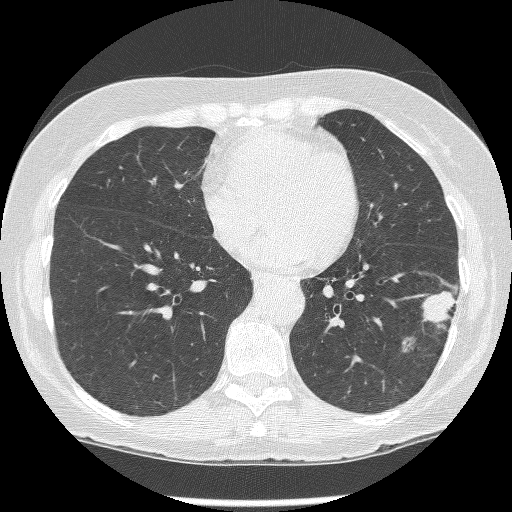
Low-dose screening chest CT, axial slice, baseline annual screen, lung window (W 1500 / L -600 HU), 1.25 mm slice thickness. Female, age 62 years at enrolment. Former smoker at enrolment.
• Lesion marked by an expert reader, bounding box <415,283,460,340> (left, top, right, bottom; pixels).
• The screening reader recorded 2 non-calcified nodules or masses ≥4 mm on this exam (left lower lobe, left lower lobe); which of them this box marks is not recorded.
• Lung cancer was diagnosed 15 days after this screen: non-small cell carcinoma, left lower lobe, stage IIIB (AJCC 6th edition), 23 mm at pathology.